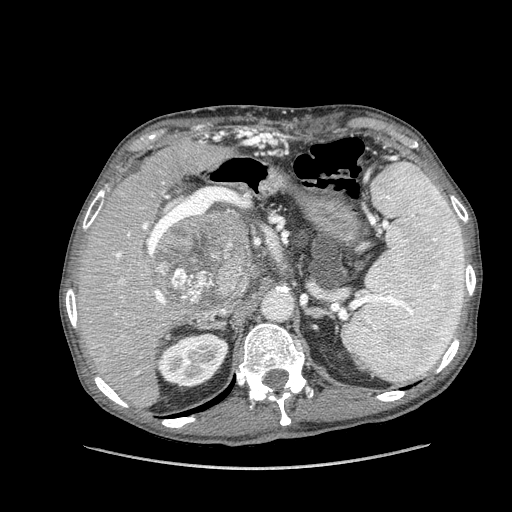
Contrast-enhanced abdominal CT (liver protocol), one axial slice. Slice 87 of 162 in the series (ordered by position). Reconstruction kernel STANDARD. 100 kVp. Soft-tissue window (W 400 / L 40 HU). 2.5 mm slice thickness. 512 × 512 image matrix, field of view 400 × 400 mm. Case-level facts recorded for this patient, not image findings: diagnosis: hepatocellular carcinoma (patient treated with transarterial chemoembolisation; whether this scan precedes or follows treatment is not stated here); TNM stage (as recorded): Stage-IIIA; Child-Pugh class: A; tumour nodularity: multinodular; tumour size: 9.9 cm.
Outlined on this slice (semi-automatic segmentation, software-assisted and operator-edited):
- liver parenchyma outside the tumour (the mass and vessels are separate outlines, so this box may not span the whole liver): bounding box <76,138,256,408> (left, top, right, bottom; pixels)
- mass: <152,208,251,311>
- liver vessels: <108,223,166,374>